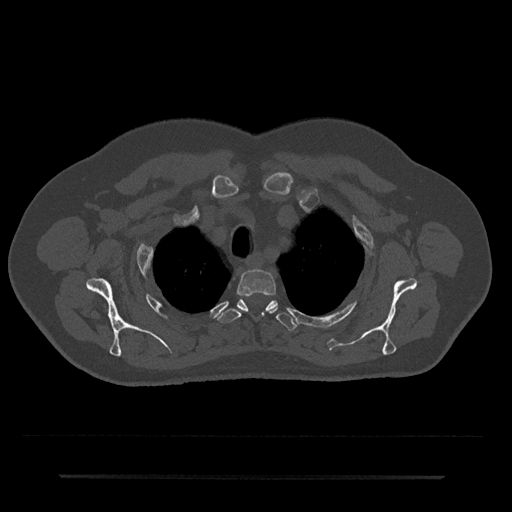
CT including the spine, one axial slice; position 585 of 797 along the scan axis; reconstruction kernel Br40s/3; bone window (W 1800 / L 400 HU); 0.5 mm slice thickness; 512 × 512 image matrix, field of view 437 × 437 mm. Male patient, age 69 years. From the clinical record (not read from this slice): primary cancer: prostate.
Annotated regions visible in this slice (semi-automatic segmentation, software-assisted and operator-edited):
- T2 vertebra: bounding box (x1, y1, x2, y2) in pixels: (237, 269, 276, 312)
- T3 vertebra: (218, 299, 298, 330)